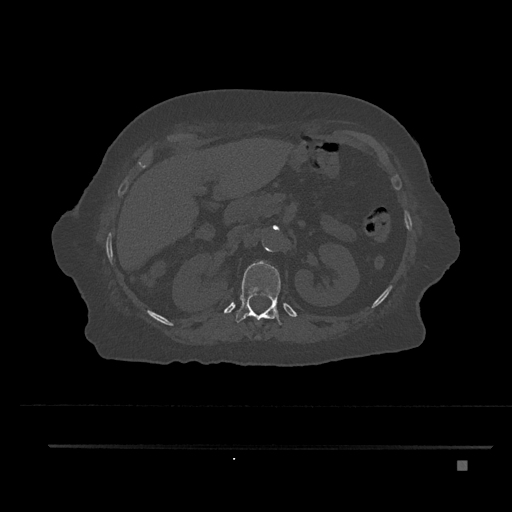
CT including the spine, one axial slice. Position 264 of 797 along the scan axis. Bone window (W 1800 / L 400 HU). 512 × 512 image matrix, field of view 437 × 437 mm. Patient: female, 76 years. Case-level facts recorded for this patient, not image findings: primary cancer: lung; vertebrae with lytic lesions (as recorded): T11, L3.
Outlined on this slice (semi-automatic segmentation, software-assisted and operator-edited):
- T12 vertebra: bounding box [x1, y1, x2, y2] px = [235, 261, 282, 337]